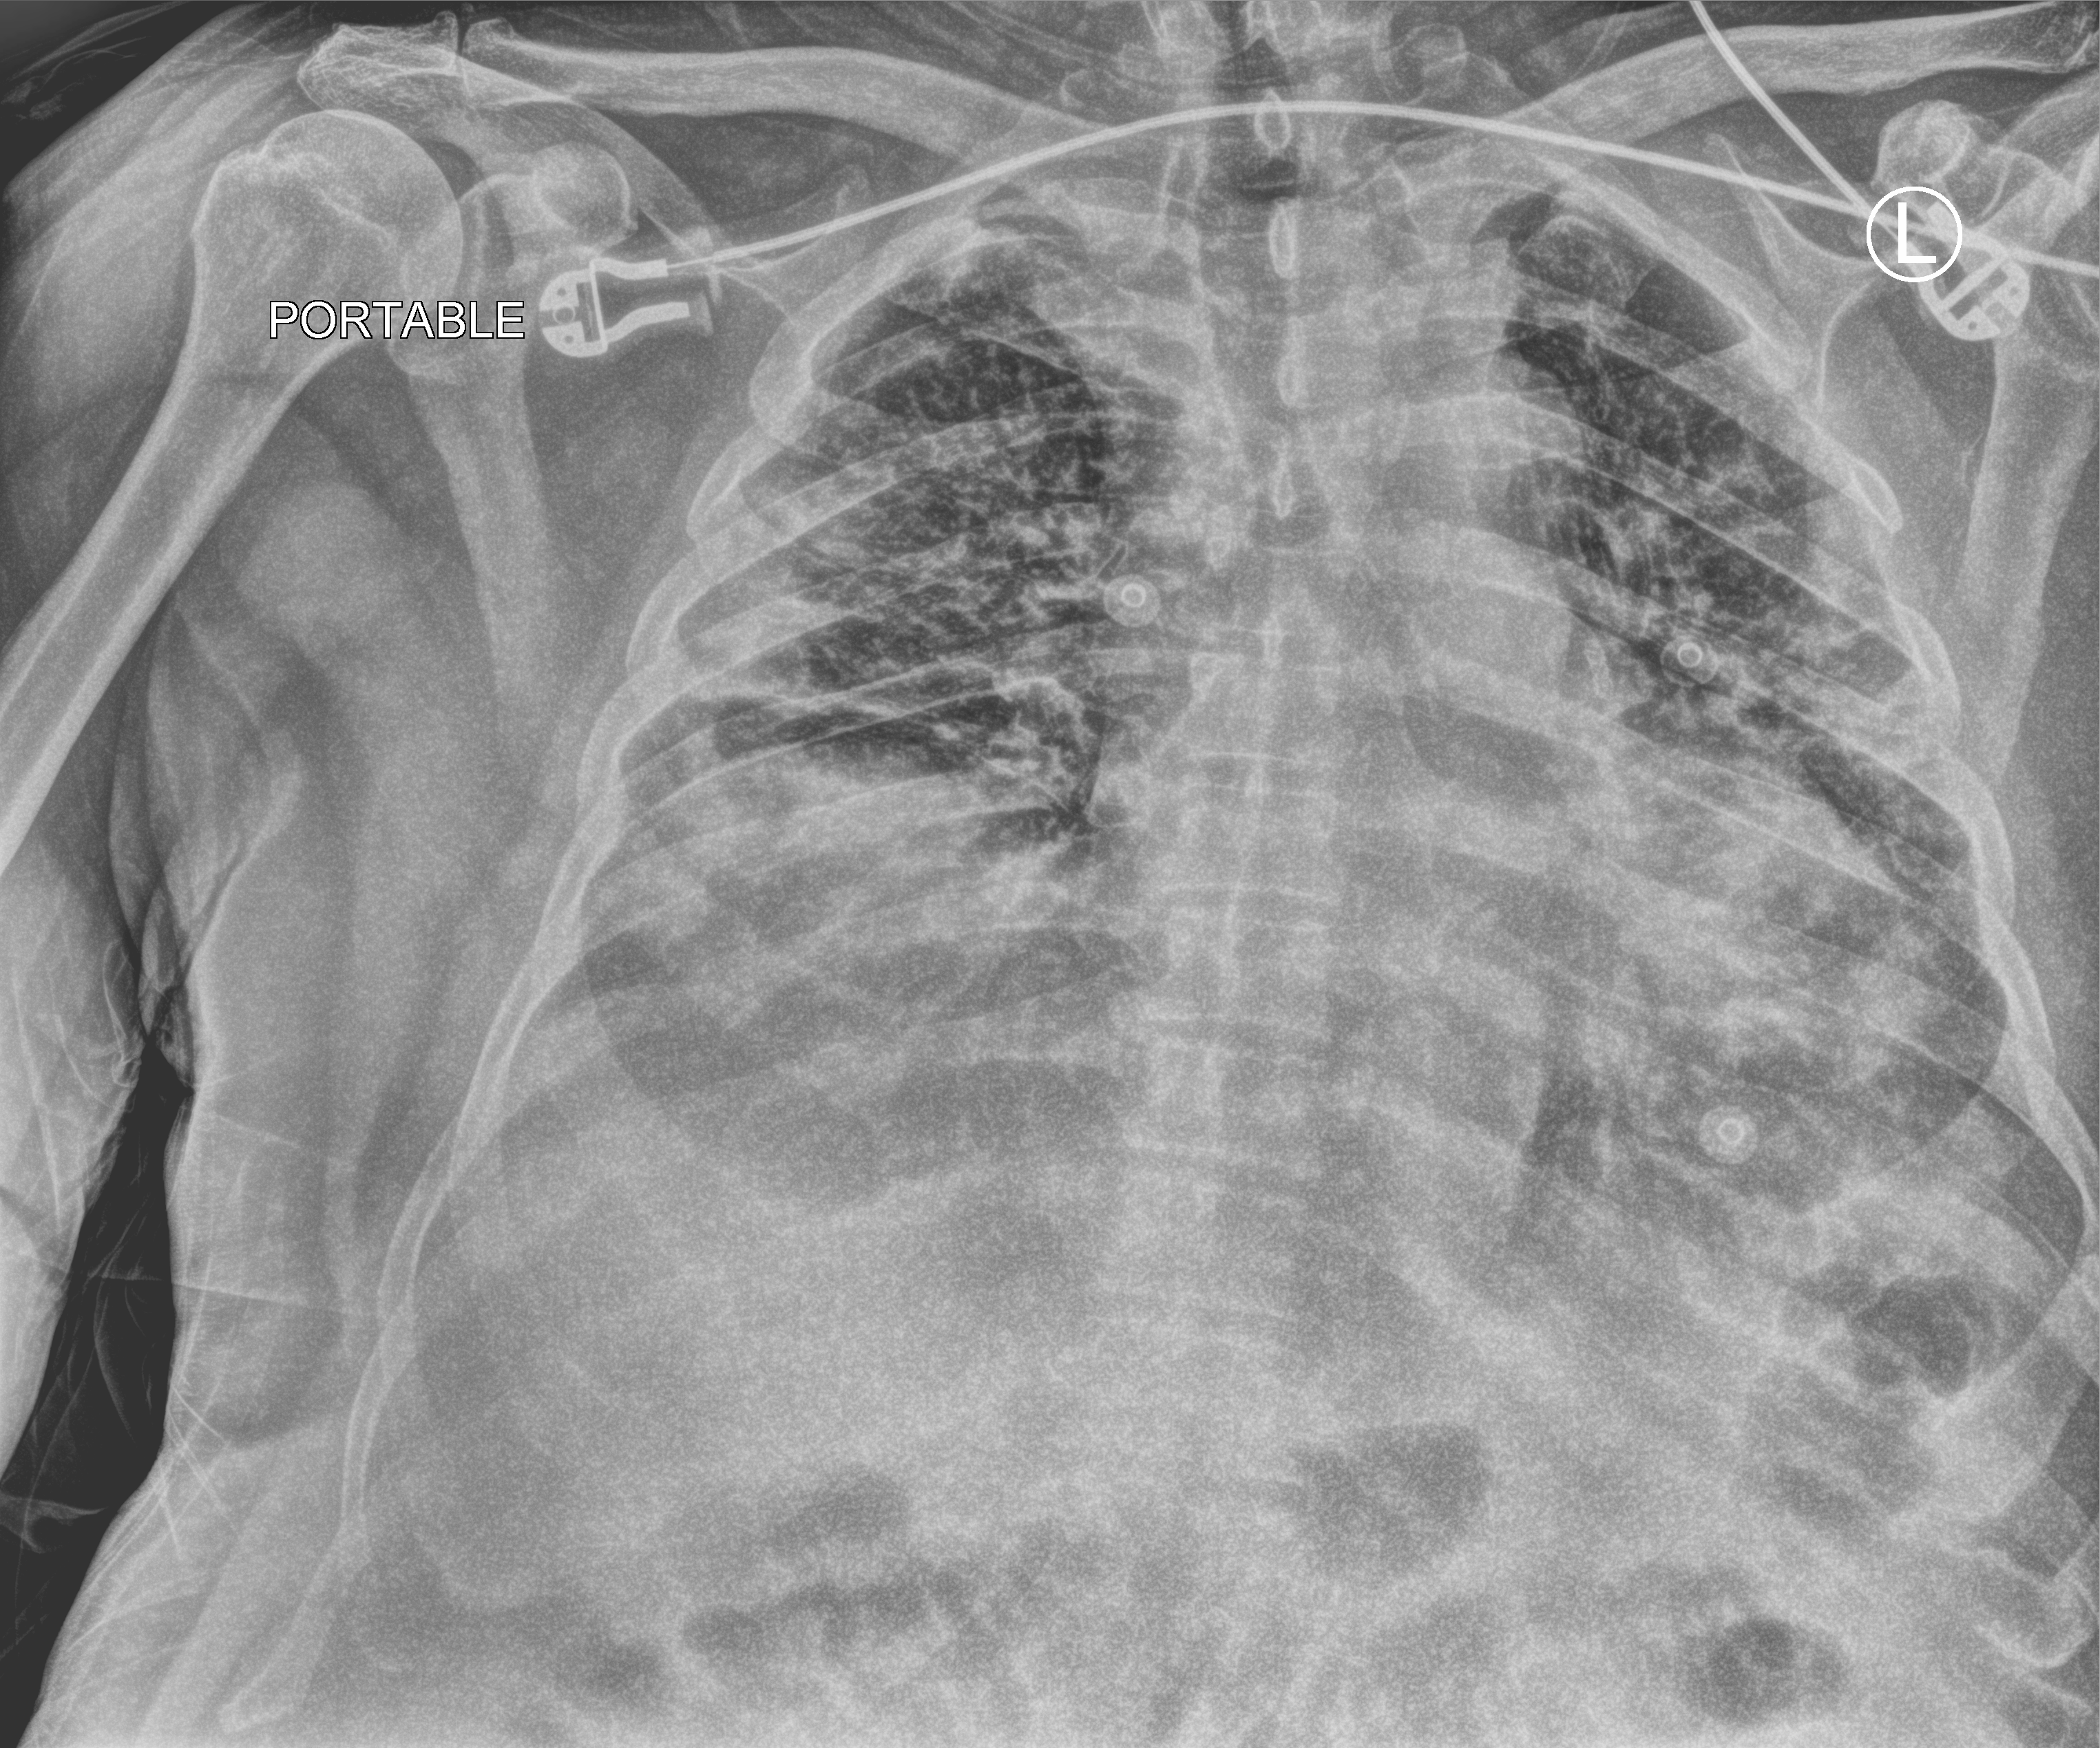
Bedside chest radiograph (computed radiography); anteroposterior (AP) projection. Patient hospitalised with COVID-19; male, aged 60–74 years.
Hospital-stay facts (about this admission, not read from this image; timing relative to this image not recorded): hypertension (admission record): yes; other chronic lung disease (admission record): no.